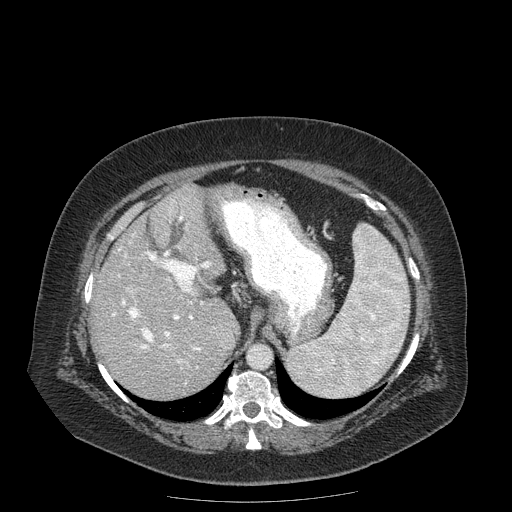
Contrast-enhanced abdominal CT (liver protocol), one axial slice; reconstruction kernel STANDARD; soft-tissue window (W 400 / L 40 HU); 2.5 mm slice thickness; 512 × 512 image matrix, field of view 440 × 440 mm. Case-level facts recorded for this patient, not image findings: diagnosis: hepatocellular carcinoma (patient treated with transarterial chemoembolisation; whether this scan precedes or follows treatment is not stated here); TNM stage (as recorded): Stage-IIIB; Child-Pugh class: A.
Outlined on this slice (semi-automatically segmented with operator editing):
- abdominal aorta: bounding box [x1, y1, x2, y2] px = [249, 345, 271, 367]
- liver parenchyma outside the tumour (the mass and vessels are separate outlines, so this box may not span the whole liver): [92, 184, 238, 398]
- liver vessels: [112, 200, 211, 368]